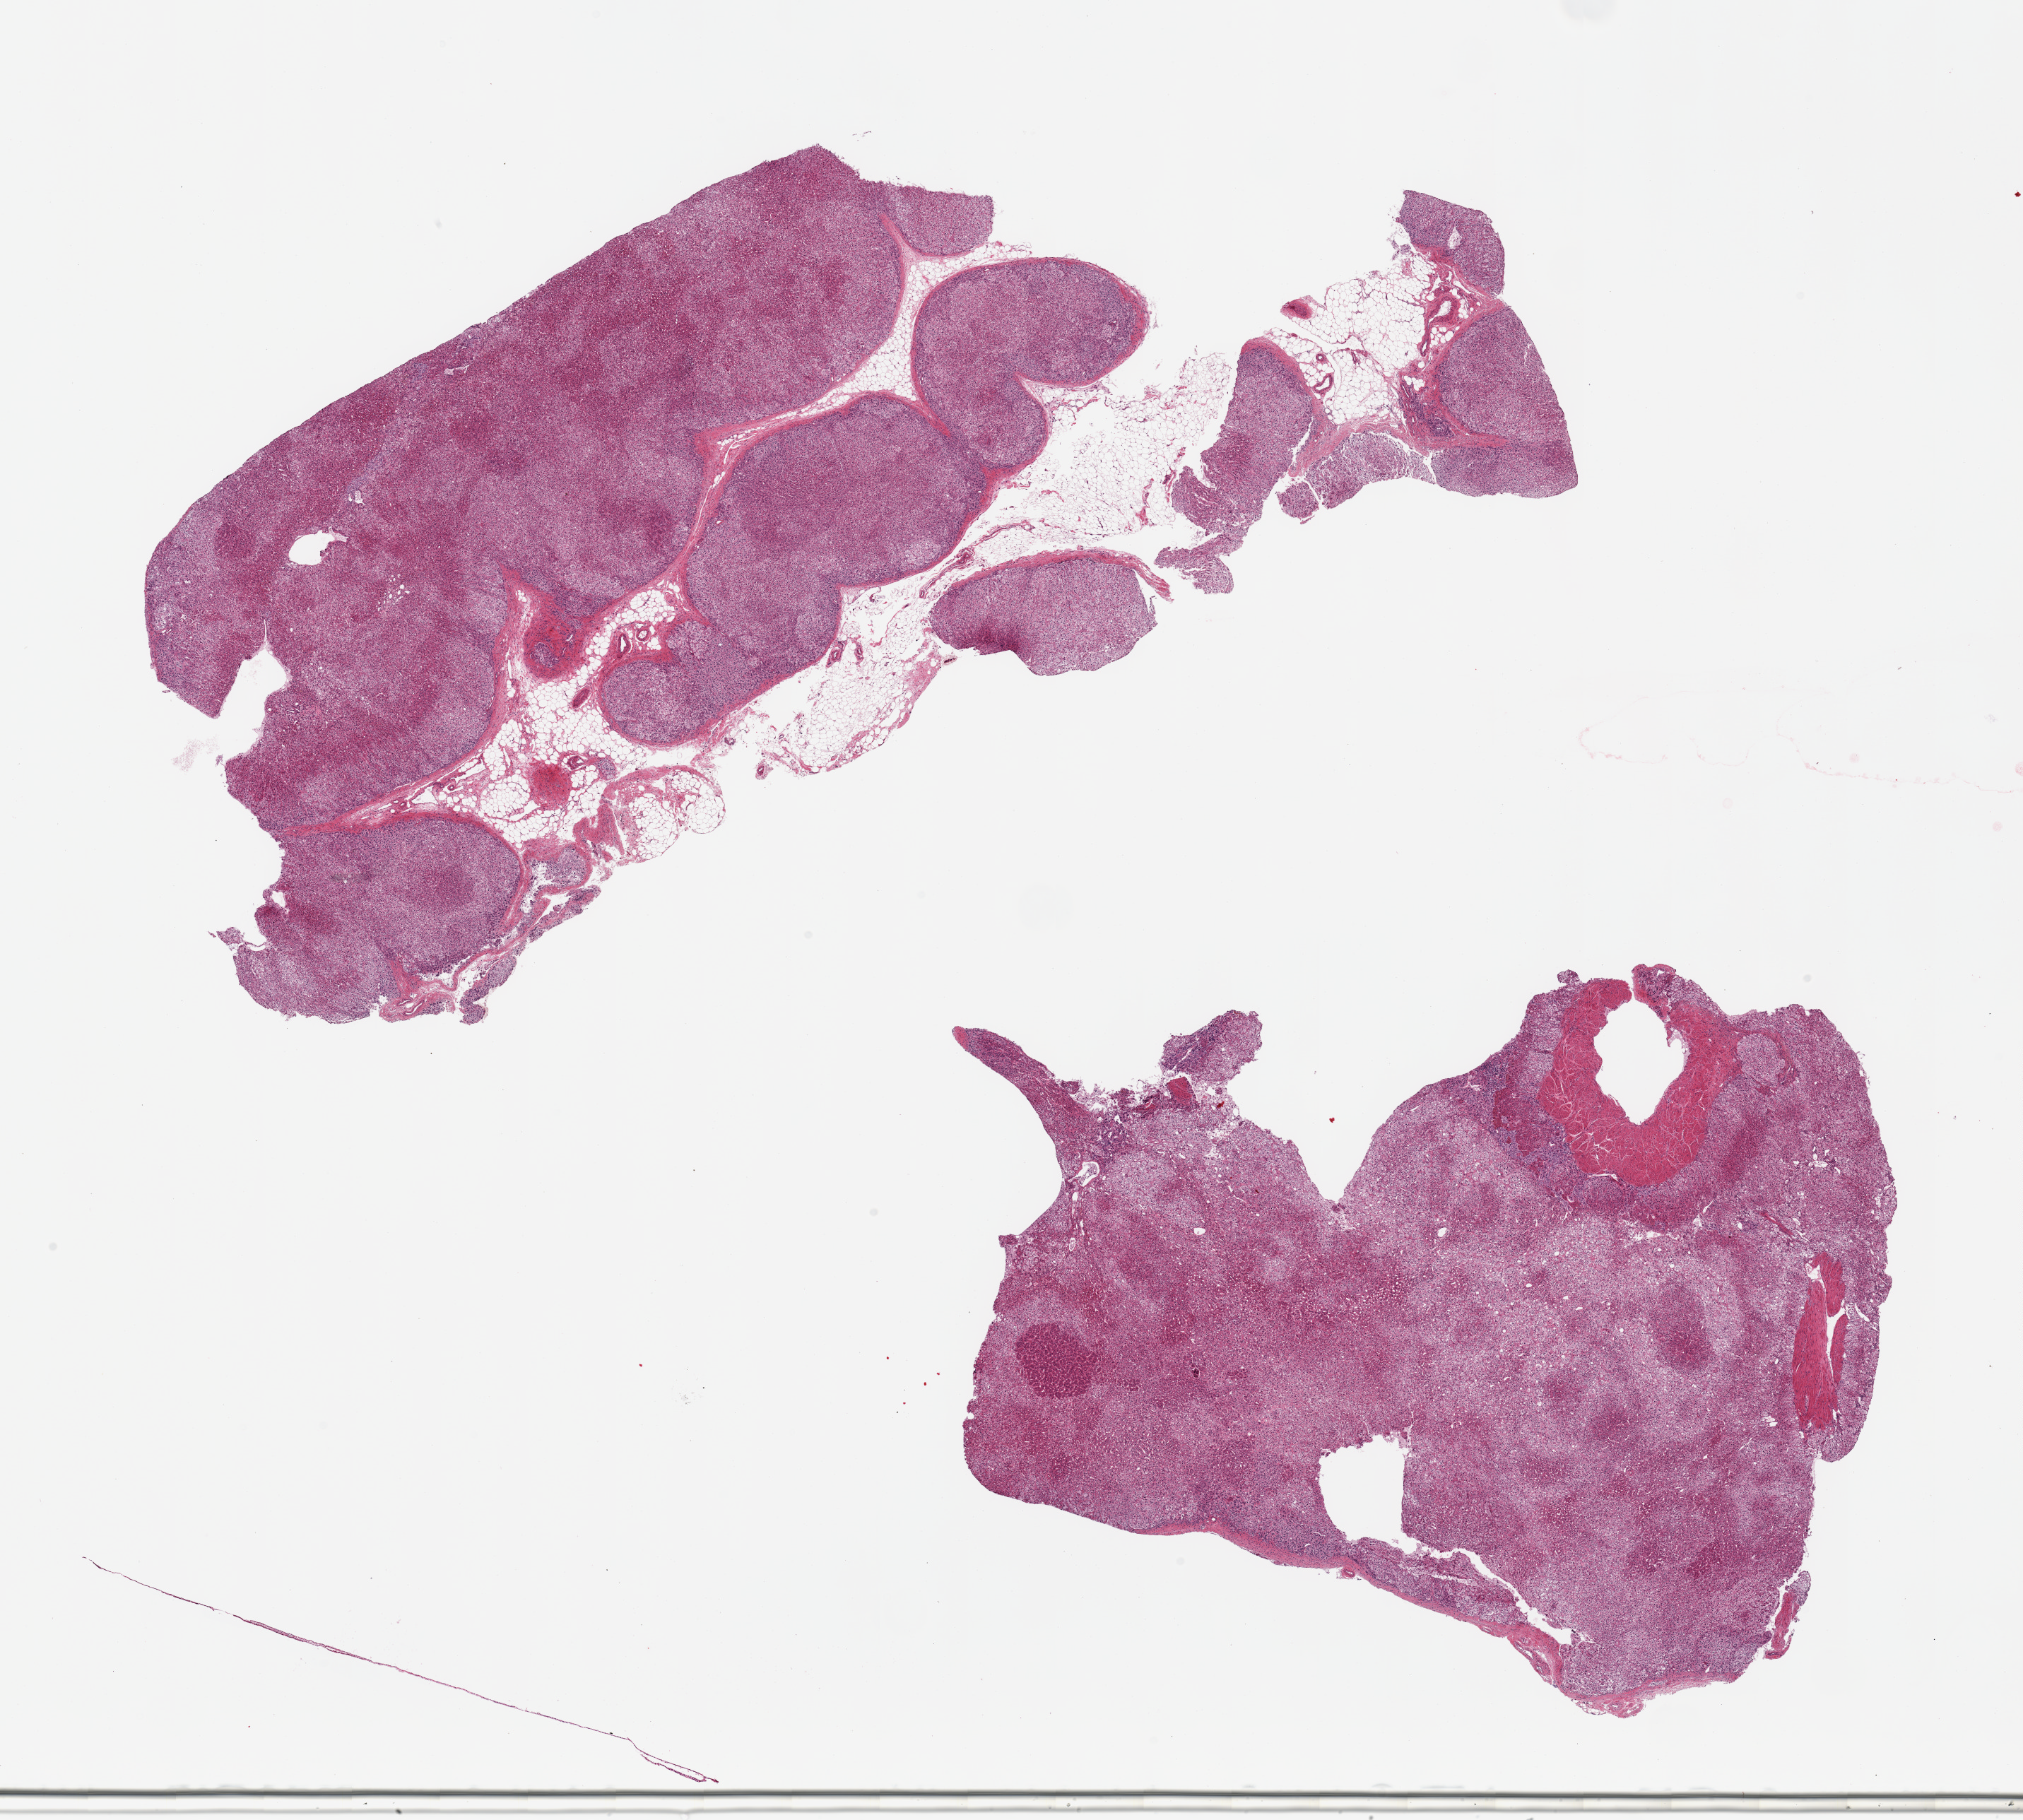
Hematoxylin and eosin (H&E) whole-slide image, low-resolution overview of the scanned area, about 22.6 x 20.4 mm (acquisition: 20x scan); PAXgene-fixed, paraffin-embedded tissue; sampled site (target tissue): adrenal gland; donor tissue sample.
Pathologist's review note for this sample: 2 pieces, all cortex, well preserved, ~10% adherent fat.